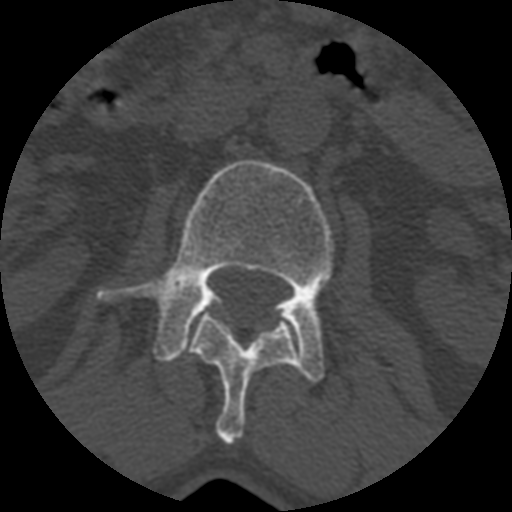
CT including the spine, one axial slice. Slice 343 of 399 in the series (ordered by position). Reconstruction kernel STANDARD. 120 kVp. Bone window (W 1800 / L 400 HU). 512 × 512 image matrix, field of view 160 × 160 mm. Patient age 71 years. From the clinical record (not read from this slice): primary cancer: prostate.
Annotated regions visible in this slice (semi-automatically segmented with operator editing):
- L1 vertebra: bounding box [x1, y1, x2, y2] px = [187, 311, 297, 445]
- L2 vertebra: [97, 159, 334, 381]